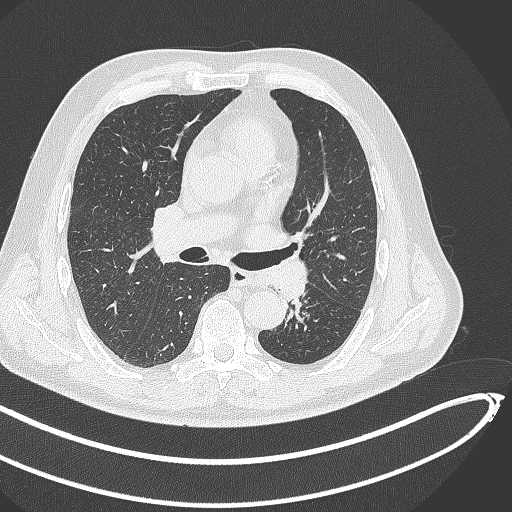
Chest CT, one axial slice; slice 269 of 468 in the series (ordered by position); reconstruction kernel B70f; 120 kVp; lung window (W 1500 / L -600 HU); 512 × 512 image matrix, field of view 400 × 400 mm. Patient: male, 64 years. Case-level facts recorded for this patient, not image findings: clinical TNM (as recorded): T1c N0 M0; histopathological grade: G2.
Outlined on this slice (bounding box drawn by a radiologist):
- lung tumour (recorded histology: squamous cell carcinoma): box from (x=261, y=250) to (x=311, y=304) px